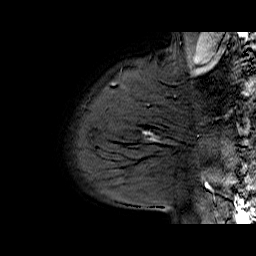
Breast MRI (dynamic contrast-enhanced), one sagittal slice. Slice 55 of 70 in the series (ordered by position). Dynamic contrast-enhanced series, time point 2 of 6 at this slice position (early post-contrast). 1.5 T. TE 6.5 ms, TR 33 ms. 4 mm slice thickness. 256 × 256 image matrix, field of view 200 × 200 mm. Female patient. Case-level facts recorded for this patient, not image findings: setting: breast cancer imaged before/during neoadjuvant chemotherapy; receptor status: HER2-positive.
Structures marked on this image (semi-automatic segmentation, software-assisted and operator-edited):
- analysis volume of interest (the breast-tissue region the enhancement analysis was run in; not a lesion): bounding box (x1, y1, x2, y2) in pixels: (113, 112, 174, 170)
- tumour enhancement mask (voxels above the 100 % enhancement threshold inside the analysis volume of interest): (143, 131, 148, 135)